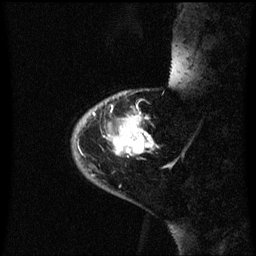
Breast MRI (dynamic contrast-enhanced), one sagittal slice. Position 11 of 60 along the scan axis. Dynamic contrast-enhanced series, image 2 of 3 at this slice position (ordered by acquisition). 1.5 T. TE 4.2 ms, TR 8.4 ms. 2.3 mm slice thickness. 256 × 256 image matrix. Female patient, age 46 years. From the clinical record (not read from this slice): setting: breast cancer imaged before/during neoadjuvant chemotherapy; receptor status: HER2-positive.
Structures marked on this image (semi-automatic segmentation, software-assisted and operator-edited):
- analysis volume of interest (the breast-tissue region the enhancement analysis was run in; not a lesion): bounding box [x1, y1, x2, y2] px = [72, 86, 173, 171]
- tumour enhancement mask (voxels above the 70 % enhancement threshold inside the analysis volume of interest): [108, 116, 153, 155]